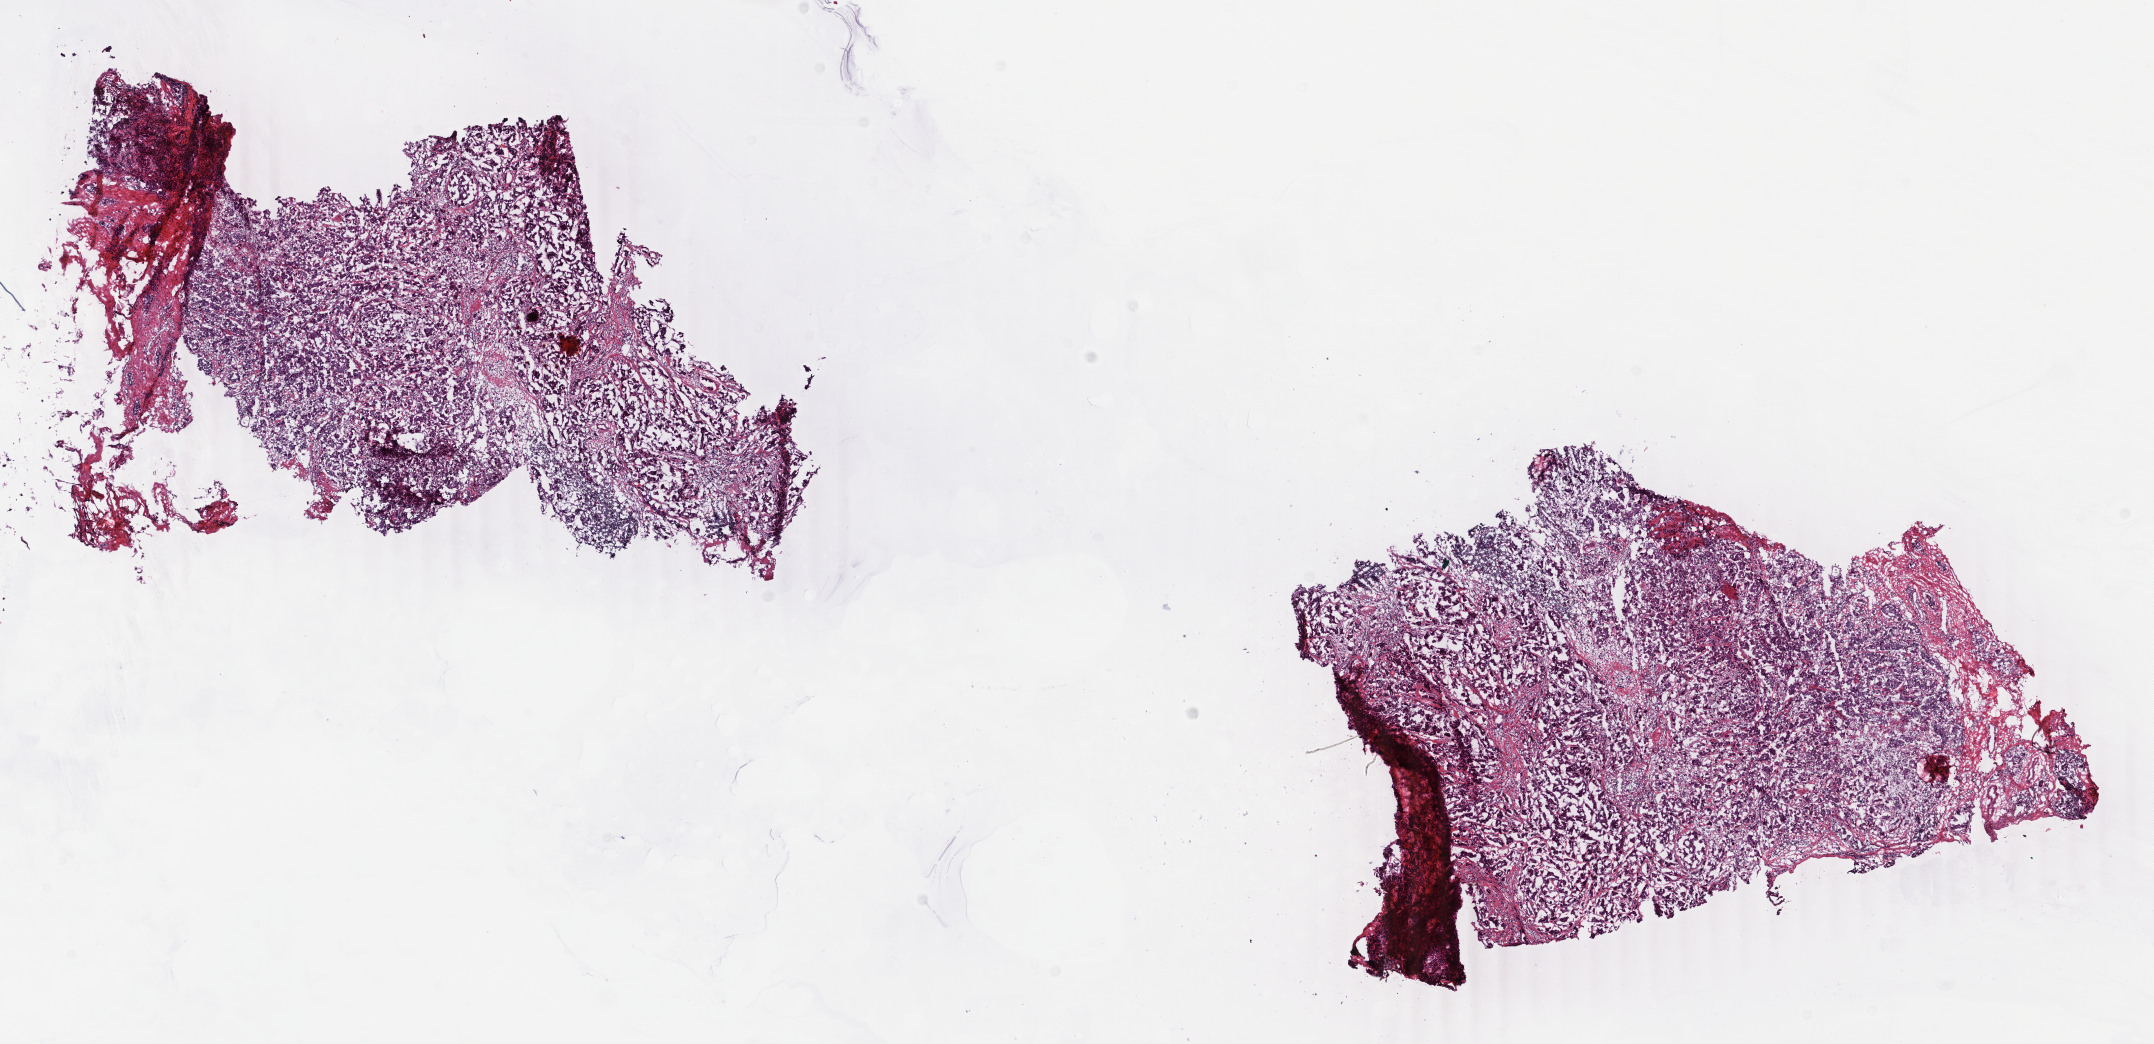
H&E-stained whole-slide image, shown as a low-resolution overview of the whole scanned area (about 17.1 x 8.3 mm, slide scanned at 40x), frozen section, primary tumour sample from the breast. Female patient; age at initial diagnosis 53 years. Composition of this section per pathologist review: tumour cells 80%, tumour nuclei 80%, normal cells 2%, stromal cells 17%, necrosis 1%. Infiltration values recorded for this section: lymphocyte infiltration 10%, monocyte infiltration 0%, neutrophil infiltration 0%.
* AJCC pathologic stage: IIB (6th edition)
* histologic diagnosis: Infiltrating duct carcinoma, NOS